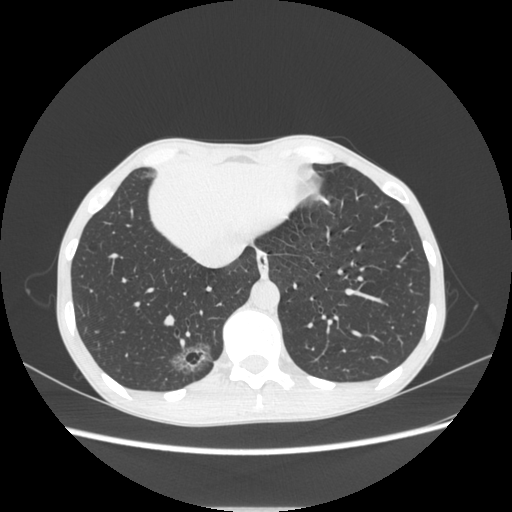
Chest CT, one axial slice. Slice 73 of 272 in the series (ordered by position). Reconstruction kernel STANDARD. Lung window (W 1500 / L -600 HU). 1.25 mm slice thickness. 512 × 512 image matrix, field of view 350 × 350 mm. Patient: female, 51 years. Case-level facts recorded for this patient, not image findings: clinical TNM (as recorded): T1c N0 M0; histopathological grade: G2-3.
Outlined on this slice (rectangle marked by the reading radiologist):
- lung tumour (recorded histology: adenocarcinoma): box from (x=157, y=333) to (x=224, y=386) px